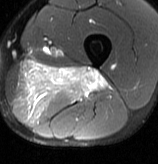
MRI of an extremity soft-tissue mass, one axial slice; position 31 of 70 along the scan axis; T2-weighted fat-saturated; MR volume resampled by the dataset authors to the PET/CT grid (not the native acquisition matrix); 3.27 mm slice thickness; 158 × 164 image matrix, field of view 154 × 160 mm. Male patient. From the clinical record (not read from this slice): histological type: extraskeletal osteosarcoma; grade: high; site of the primary tumour: left adductur.
Structures marked on this image (expert contour drawn on MRI and transferred to this co-registered scan by the dataset authors):
- gross tumour volume (mass): bounding box <13,60,110,124> (left, top, right, bottom; pixels)